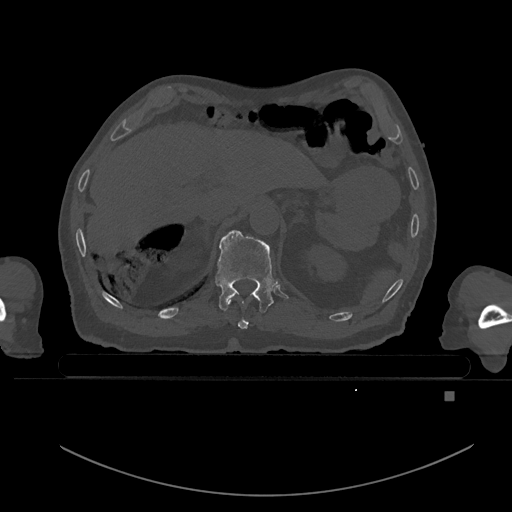
CT including the spine, one axial slice; bone window (W 1800 / L 400 HU); 0.5 mm slice thickness; 512 × 512 image matrix. Patient: male, 82 years. Case-level facts recorded for this patient, not image findings: primary cancer: prostate; vertebrae with lytic lesions (as recorded): T11, T9, T8, T2.
Structures marked on this image (semi-automatically segmented with operator editing):
- T10 vertebra: bounding box [x1, y1, x2, y2] px = [228, 301, 248, 330]
- T11 vertebra: [215, 230, 278, 313]